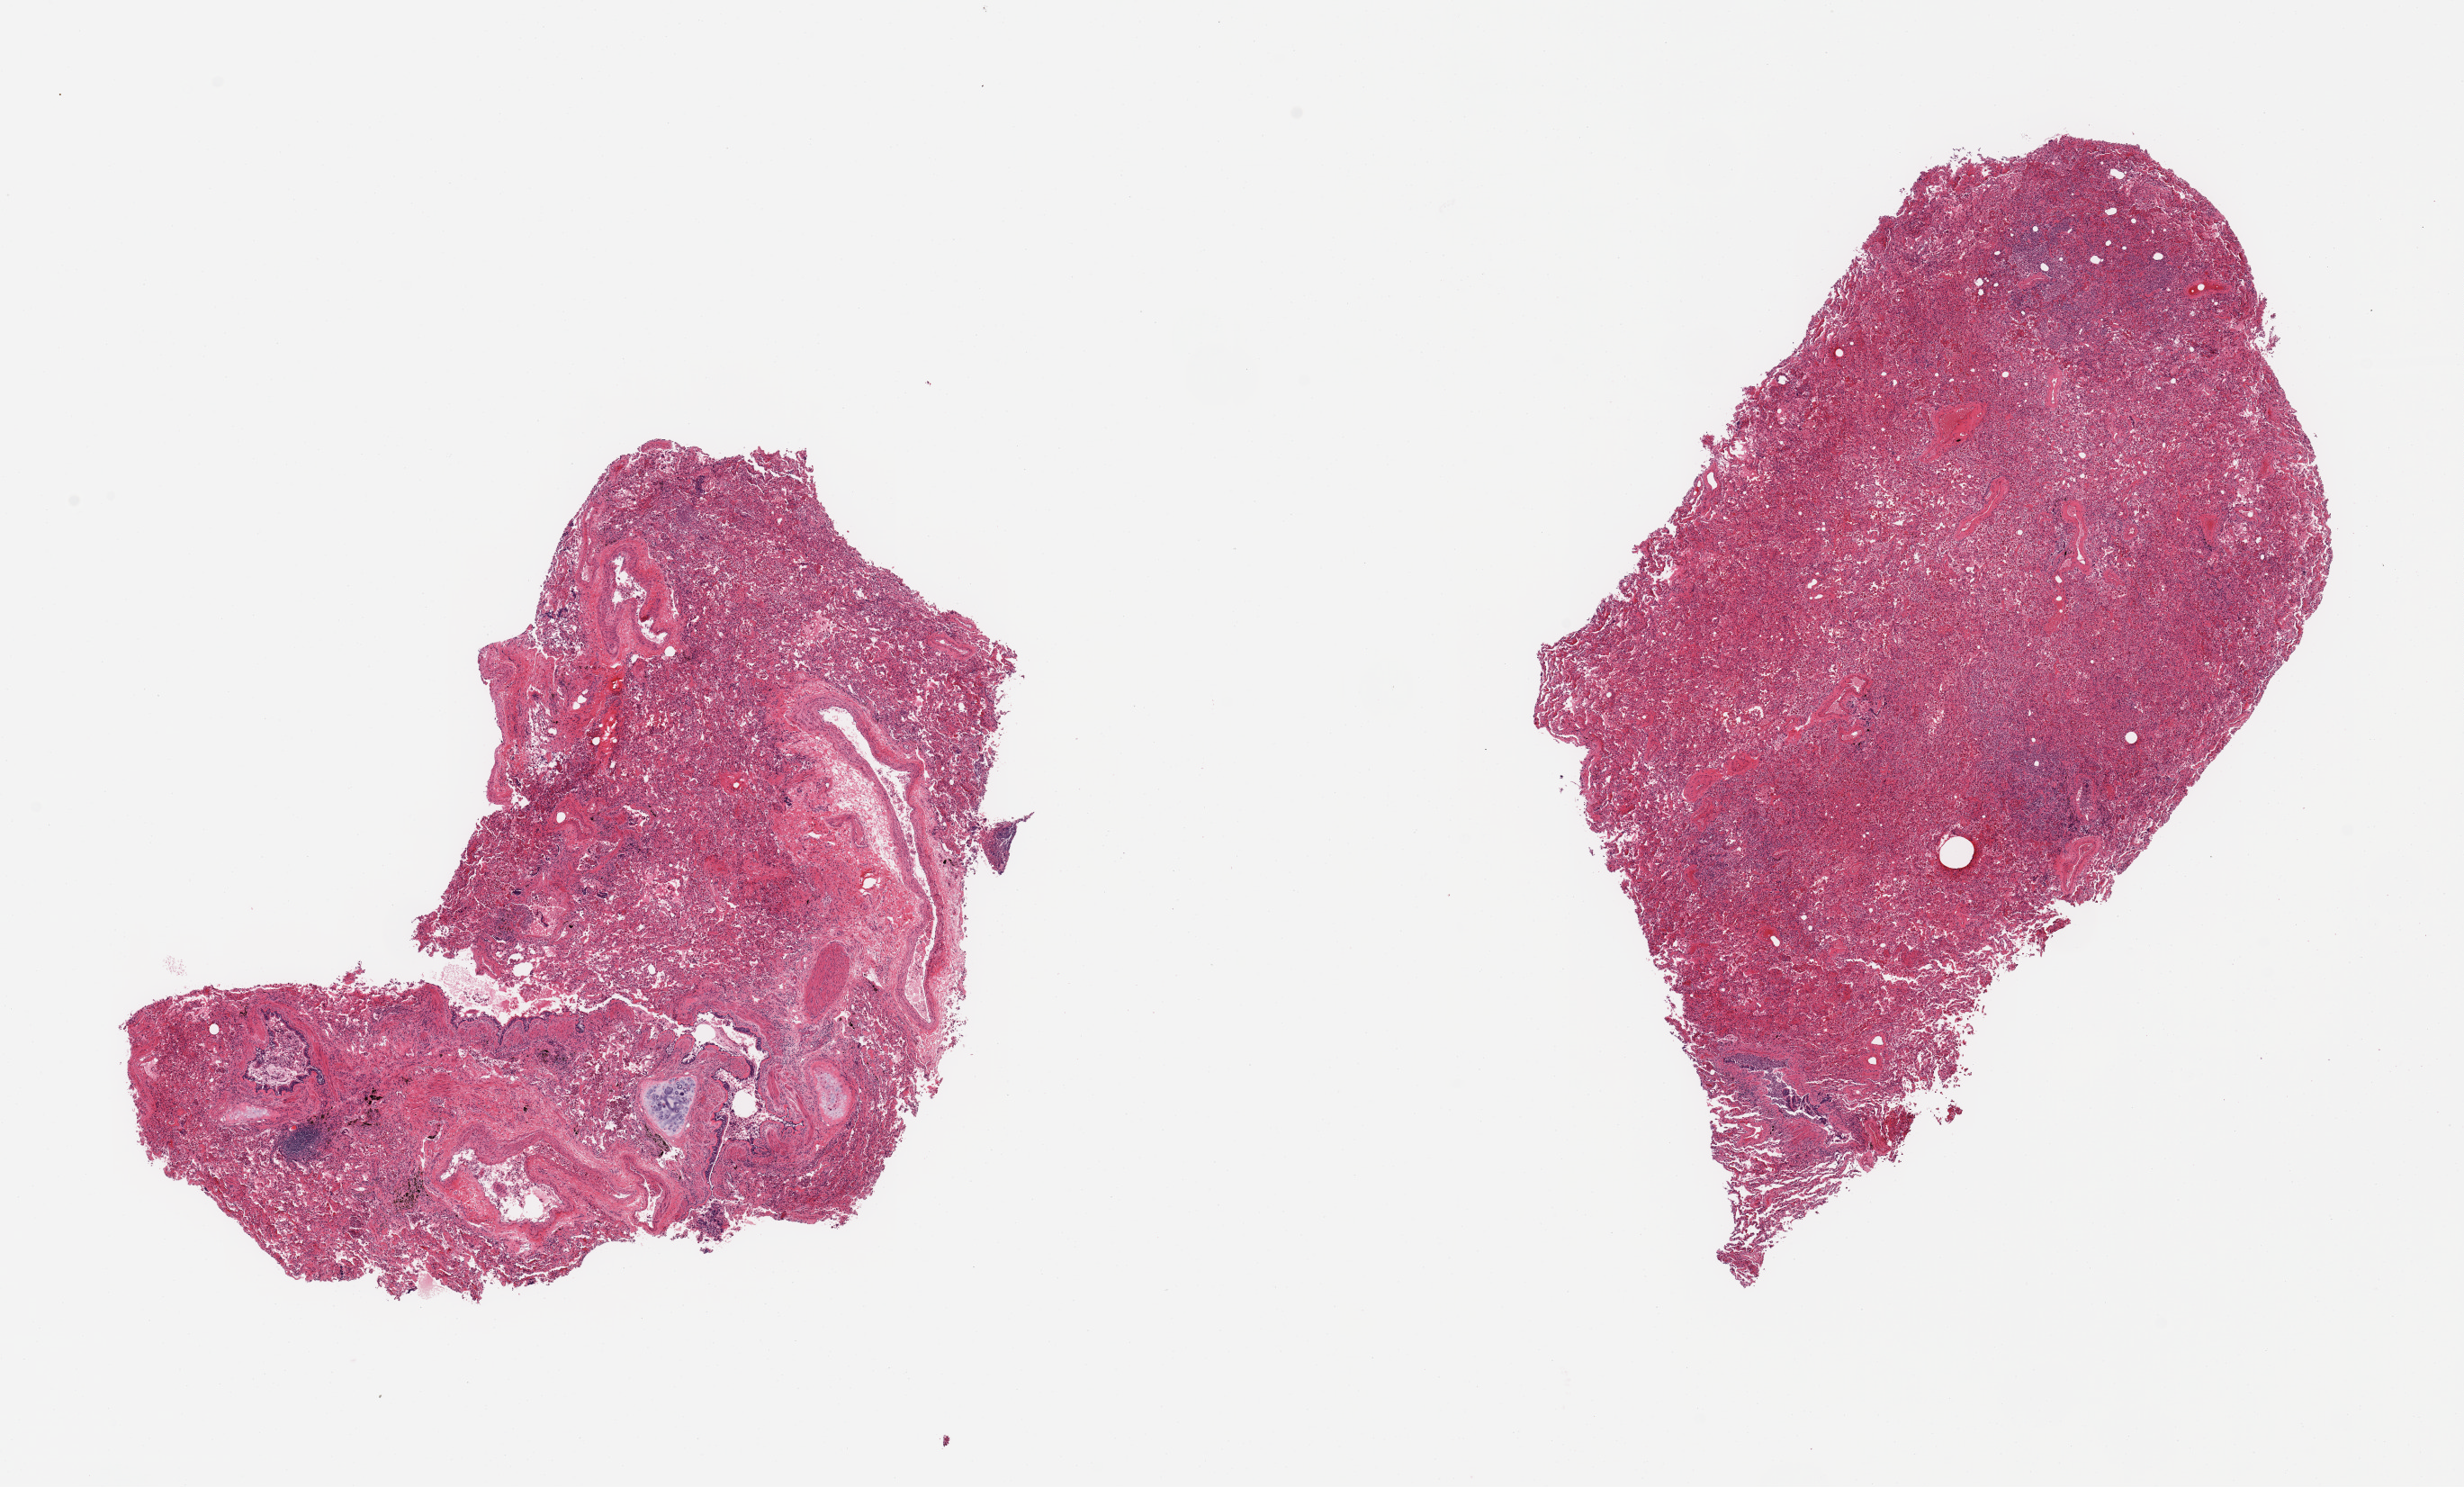
Whole-slide image, H&E stain — shown as a low-resolution overview of the whole scanned area (about 21.7 x 13.1 mm). PAXgene-fixed, paraffin-embedded tissue. Section of lung (target tissue). Tissue donor sample. Donor sex: female.
* review note (as recorded): 2 pieces; includes portion of larger bronchi/vessels/cartilage (not target), bronchopneumonia, some thickening of basement membrane and smooth muscle hypertrophy